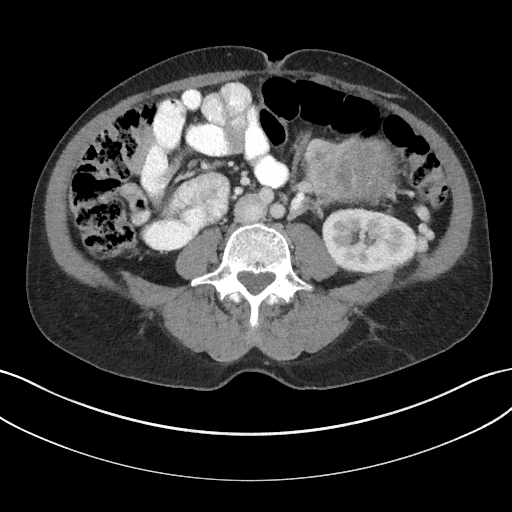
Contrast-enhanced abdominal CT, one axial slice. Position 74 of 147 along the scan axis. Reconstruction kernel I31f/3. Intravenous contrast given. Soft-tissue window (W 400 / L 40 HU). 3 mm slice thickness. 512 × 512 image matrix, field of view 384 × 384 mm. Male patient, age 58 years. Case-level facts recorded for this patient, not image findings: diagnosis: adrenocortical carcinoma; tumour side: left adrenal; tumour size at pathology: 22 cm; Ki-67 index: 26 %; stage (as recorded): 2.
Annotated regions visible in this slice (semi-automatically segmented with operator editing):
- mass: box from (x=310, y=138) to (x=394, y=203) px